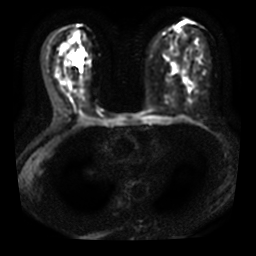
Breast MRI, one axial slice. Position 18 of 40 along the scan axis. Diffusion-weighted series; image 2 of 4 stored at this slice position (different b-values; order by instance number). 3 T. 5 mm slice thickness. 256 × 256 image matrix. Female patient.
Annotated regions visible in this slice (expert manual segmentation):
- tumour on diffusion-weighted imaging: bounding box <72,54,83,66> (left, top, right, bottom; pixels)